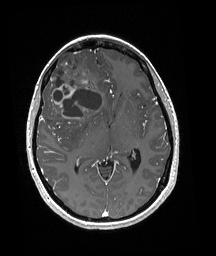
Brain MRI from a brain-tumour surgery series, one axial slice; position 102 of 192 along the scan axis; T1-weighted post-contrast; 1 mm slice thickness; 216 × 256 image matrix, field of view 211 × 250 mm. Case-level facts recorded for this patient, not image findings: histopathology: Oligodendroglioma; WHO grade: 3; IDH mutation: yes.
Outlined on this slice (expert manual segmentation):
- tumour: box from (x=48, y=52) to (x=102, y=118) px